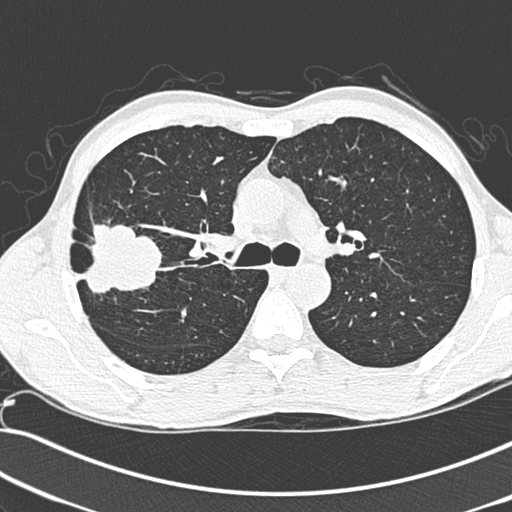
Low-dose screening chest CT, one axial slice; position 198 of 281 along the scan axis; lung window (W 1500 / L -600 HU); 1.3 mm slice thickness; 512 × 512 image matrix, field of view 341 × 341 mm.
Annotated regions visible in this slice (expert manual segmentation):
- lesion 1 (tumor, upper lobe of right lung): bounding box (x1, y1, x2, y2) in pixels: (80, 218, 162, 294)